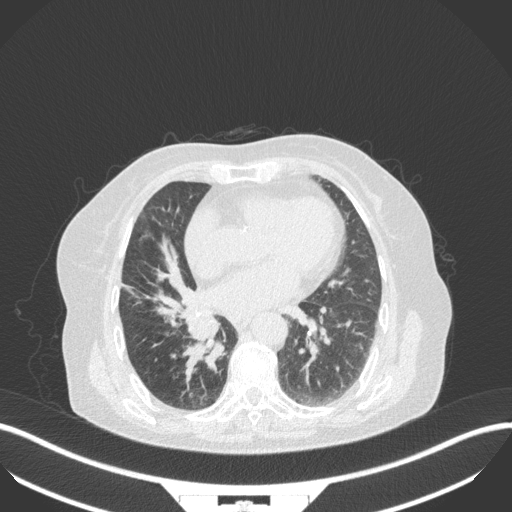
Chest CT, one axial slice. Position 133 of 329 along the scan axis. Reconstruction kernel B31f. 120 kVp. Lung window (W 1500 / L -600 HU). 1 mm slice thickness. 512 × 512 image matrix, field of view 400 × 400 mm. Patient: female, 75 years. From the clinical record (not read from this slice): clinical TNM (as recorded): T1b N0 M1a.
Structures marked on this image (rectangle marked by the reading radiologist):
- lung tumour (recorded histology: squamous cell carcinoma): bounding box (x1, y1, x2, y2) in pixels: (176, 312, 226, 382)